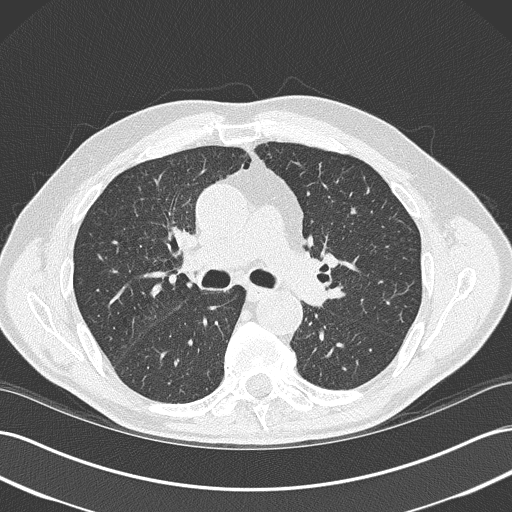
Axial slice from a low-dose chest CT screening exam; baseline screening round; lung window (W 1500 / L -600 HU); 2 mm slice thickness; lung (sharp) reconstruction kernel (B50f); 512 × 512 image matrix, field of view 360 × 360 mm. Male participant, aged 73 years at enrolment.
Expert-annotated lung lesion, bounding box <334,196,373,234> (left, top, right, bottom; pixels). The screening reader recorded 2 non-calcified nodules or masses ≥4 mm on this exam (right lower lobe, left upper lobe); which of them this box marks is not recorded. Official screen result: positive, change unspecified: nodule(s) >= 4 mm or enlarging nodule(s), mass(es), or other non-specific abnormalities suspicious for lung cancer. Lung cancer was diagnosed 400 days after this screen: small cell carcinoma, NOS, left upper lobe, stage IIIB (AJCC 6th edition), 19 mm at pathology.